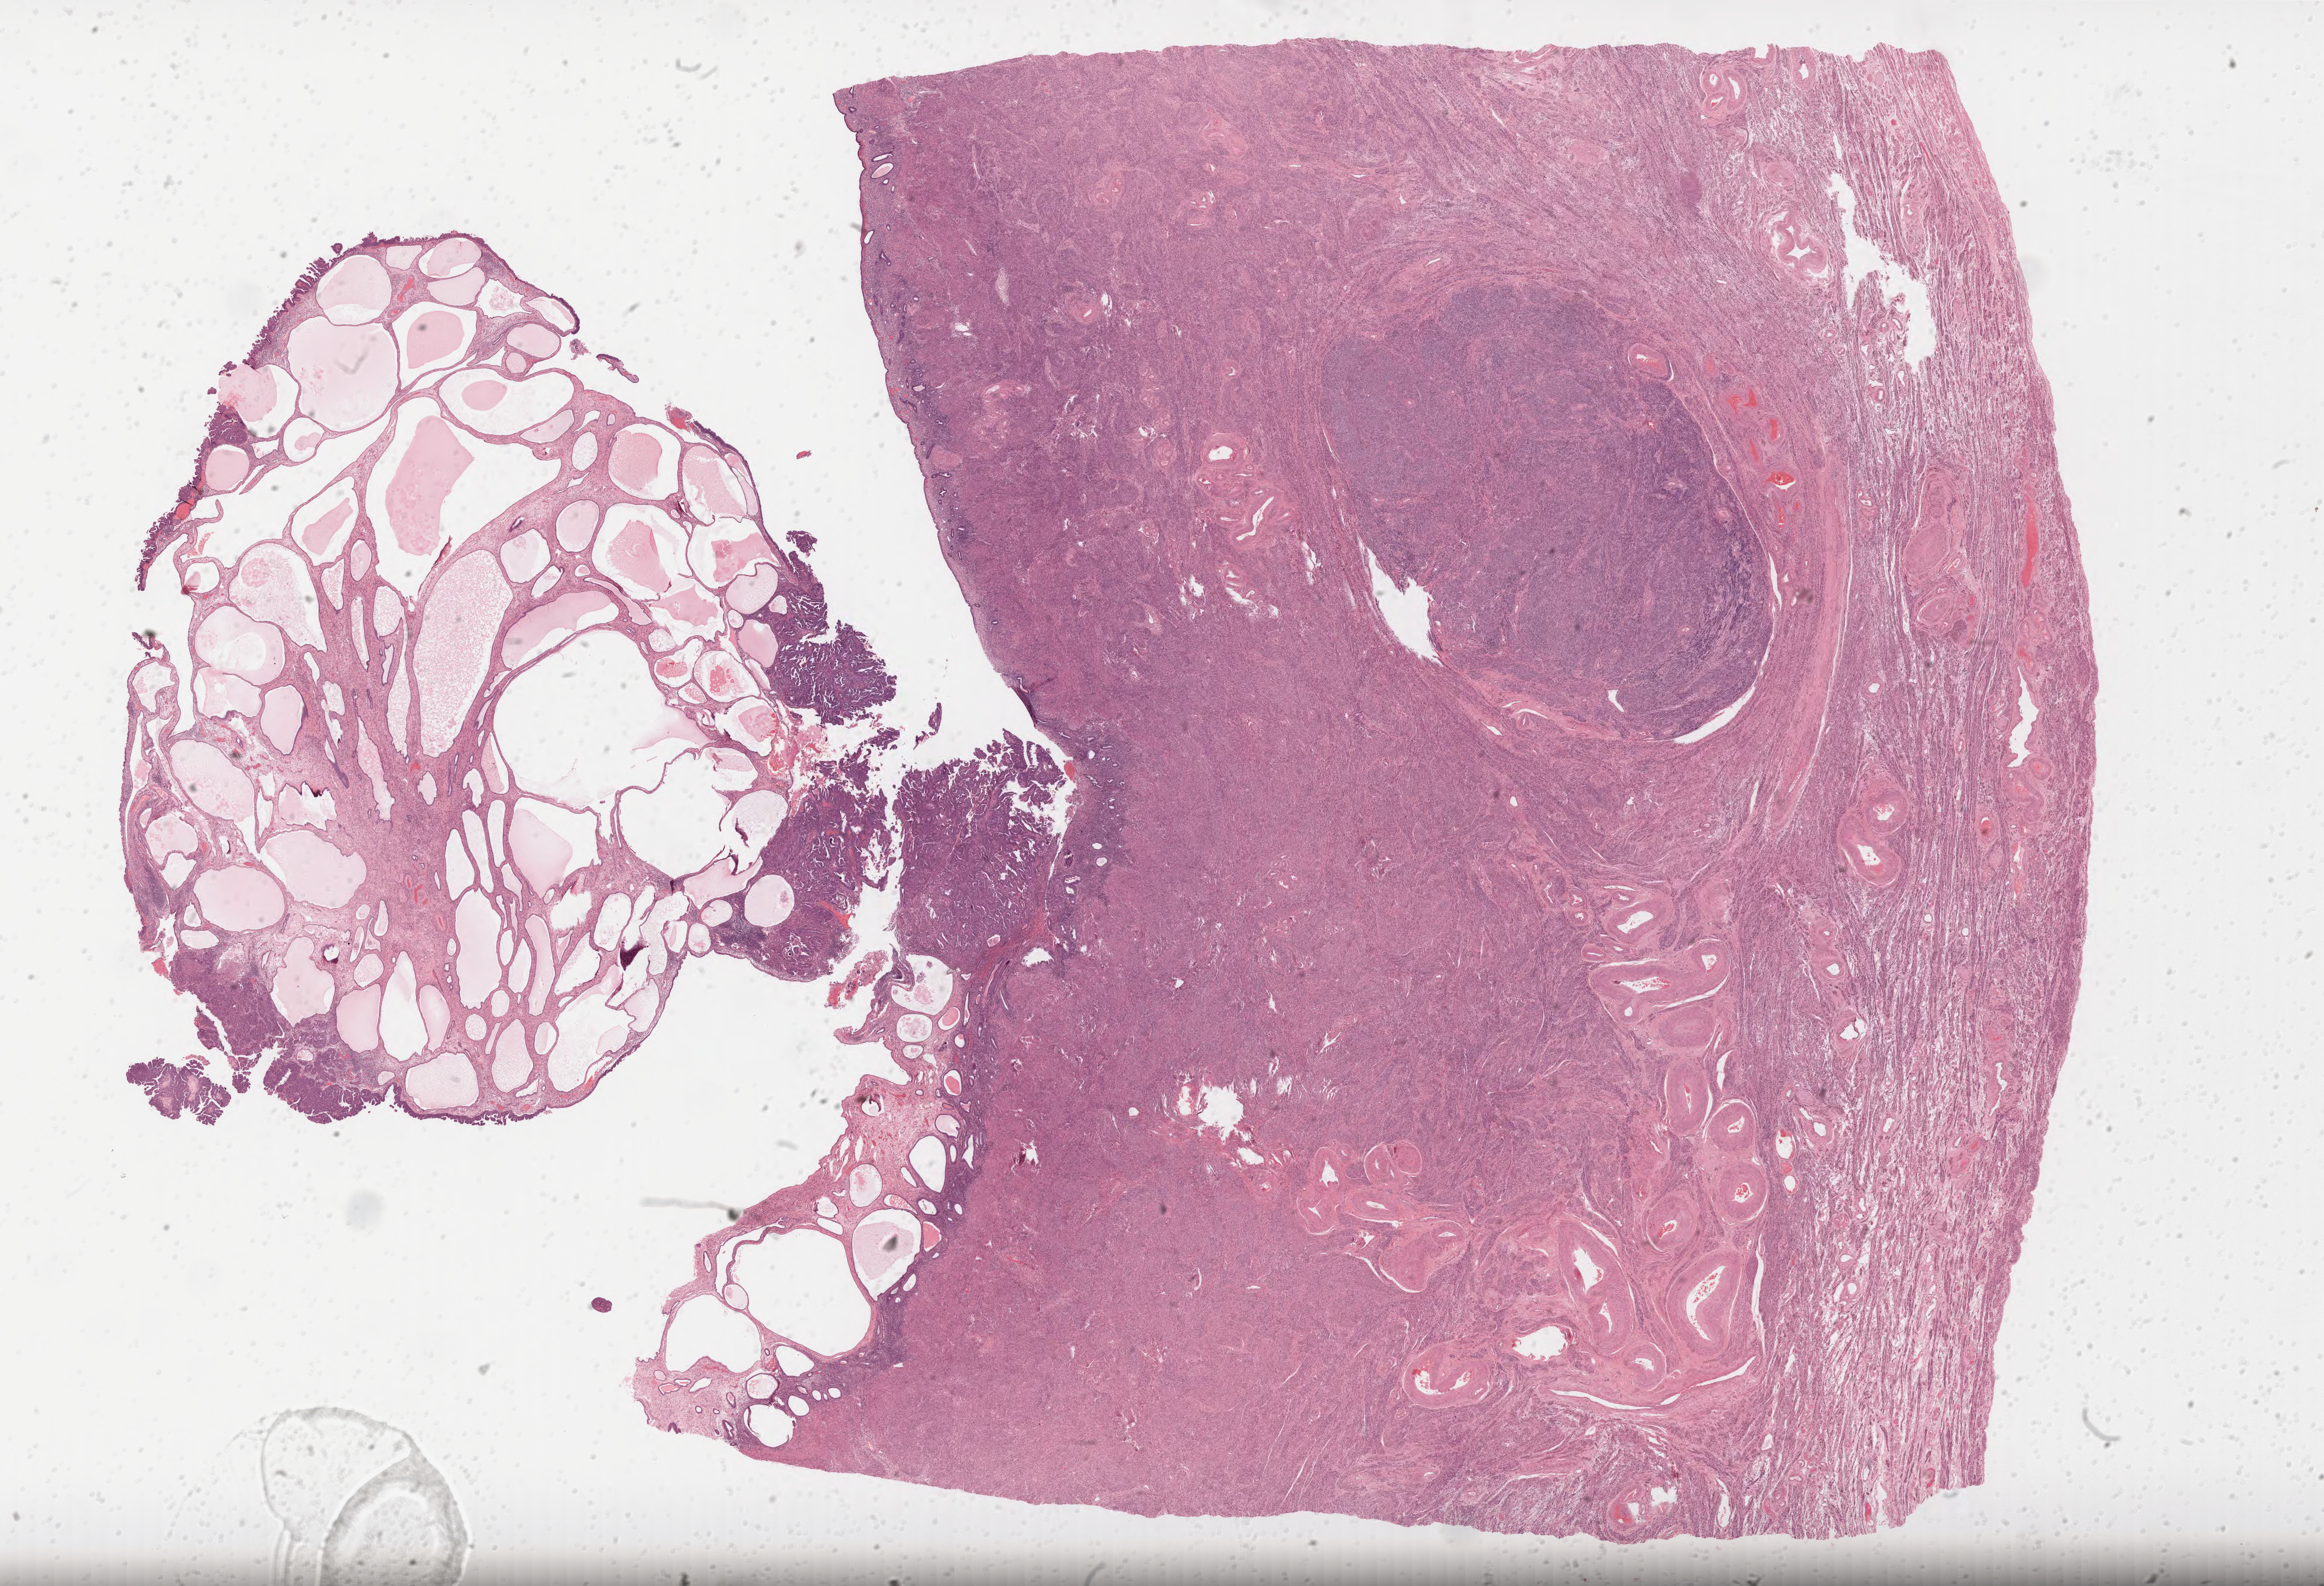
H&E-stained whole-slide image, low-resolution overview of the scanned area, about 31.7 x 21.6 mm (acquisition: 40x scan), formalin-fixed paraffin-embedded (FFPE) diagnostic section, uterus, primary tumour sample. Female, age 68 years at initial diagnosis. Histologic grade: G3 (poorly differentiated).
- FIGO stage: II
- diagnosis: Serous cystadenocarcinoma, NOS (endometrium)